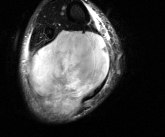
MRI of an extremity soft-tissue mass, one axial slice; position 41 of 81 along the scan axis; T2-weighted fat-saturated; MR volume resampled by the dataset authors to the PET/CT grid (not the native acquisition matrix); 3.27 mm slice thickness; 165 × 137 image matrix, field of view 161 × 134 mm. Male patient. From the clinical record (not read from this slice): histological type: liposarcoma - round cell; grade: high; site of the primary tumour: right calf.
Structures marked on this image (expert contour drawn on MRI and transferred to this co-registered scan by the dataset authors):
- gross tumour volume (mass): bounding box [x1, y1, x2, y2] px = [28, 30, 109, 115]